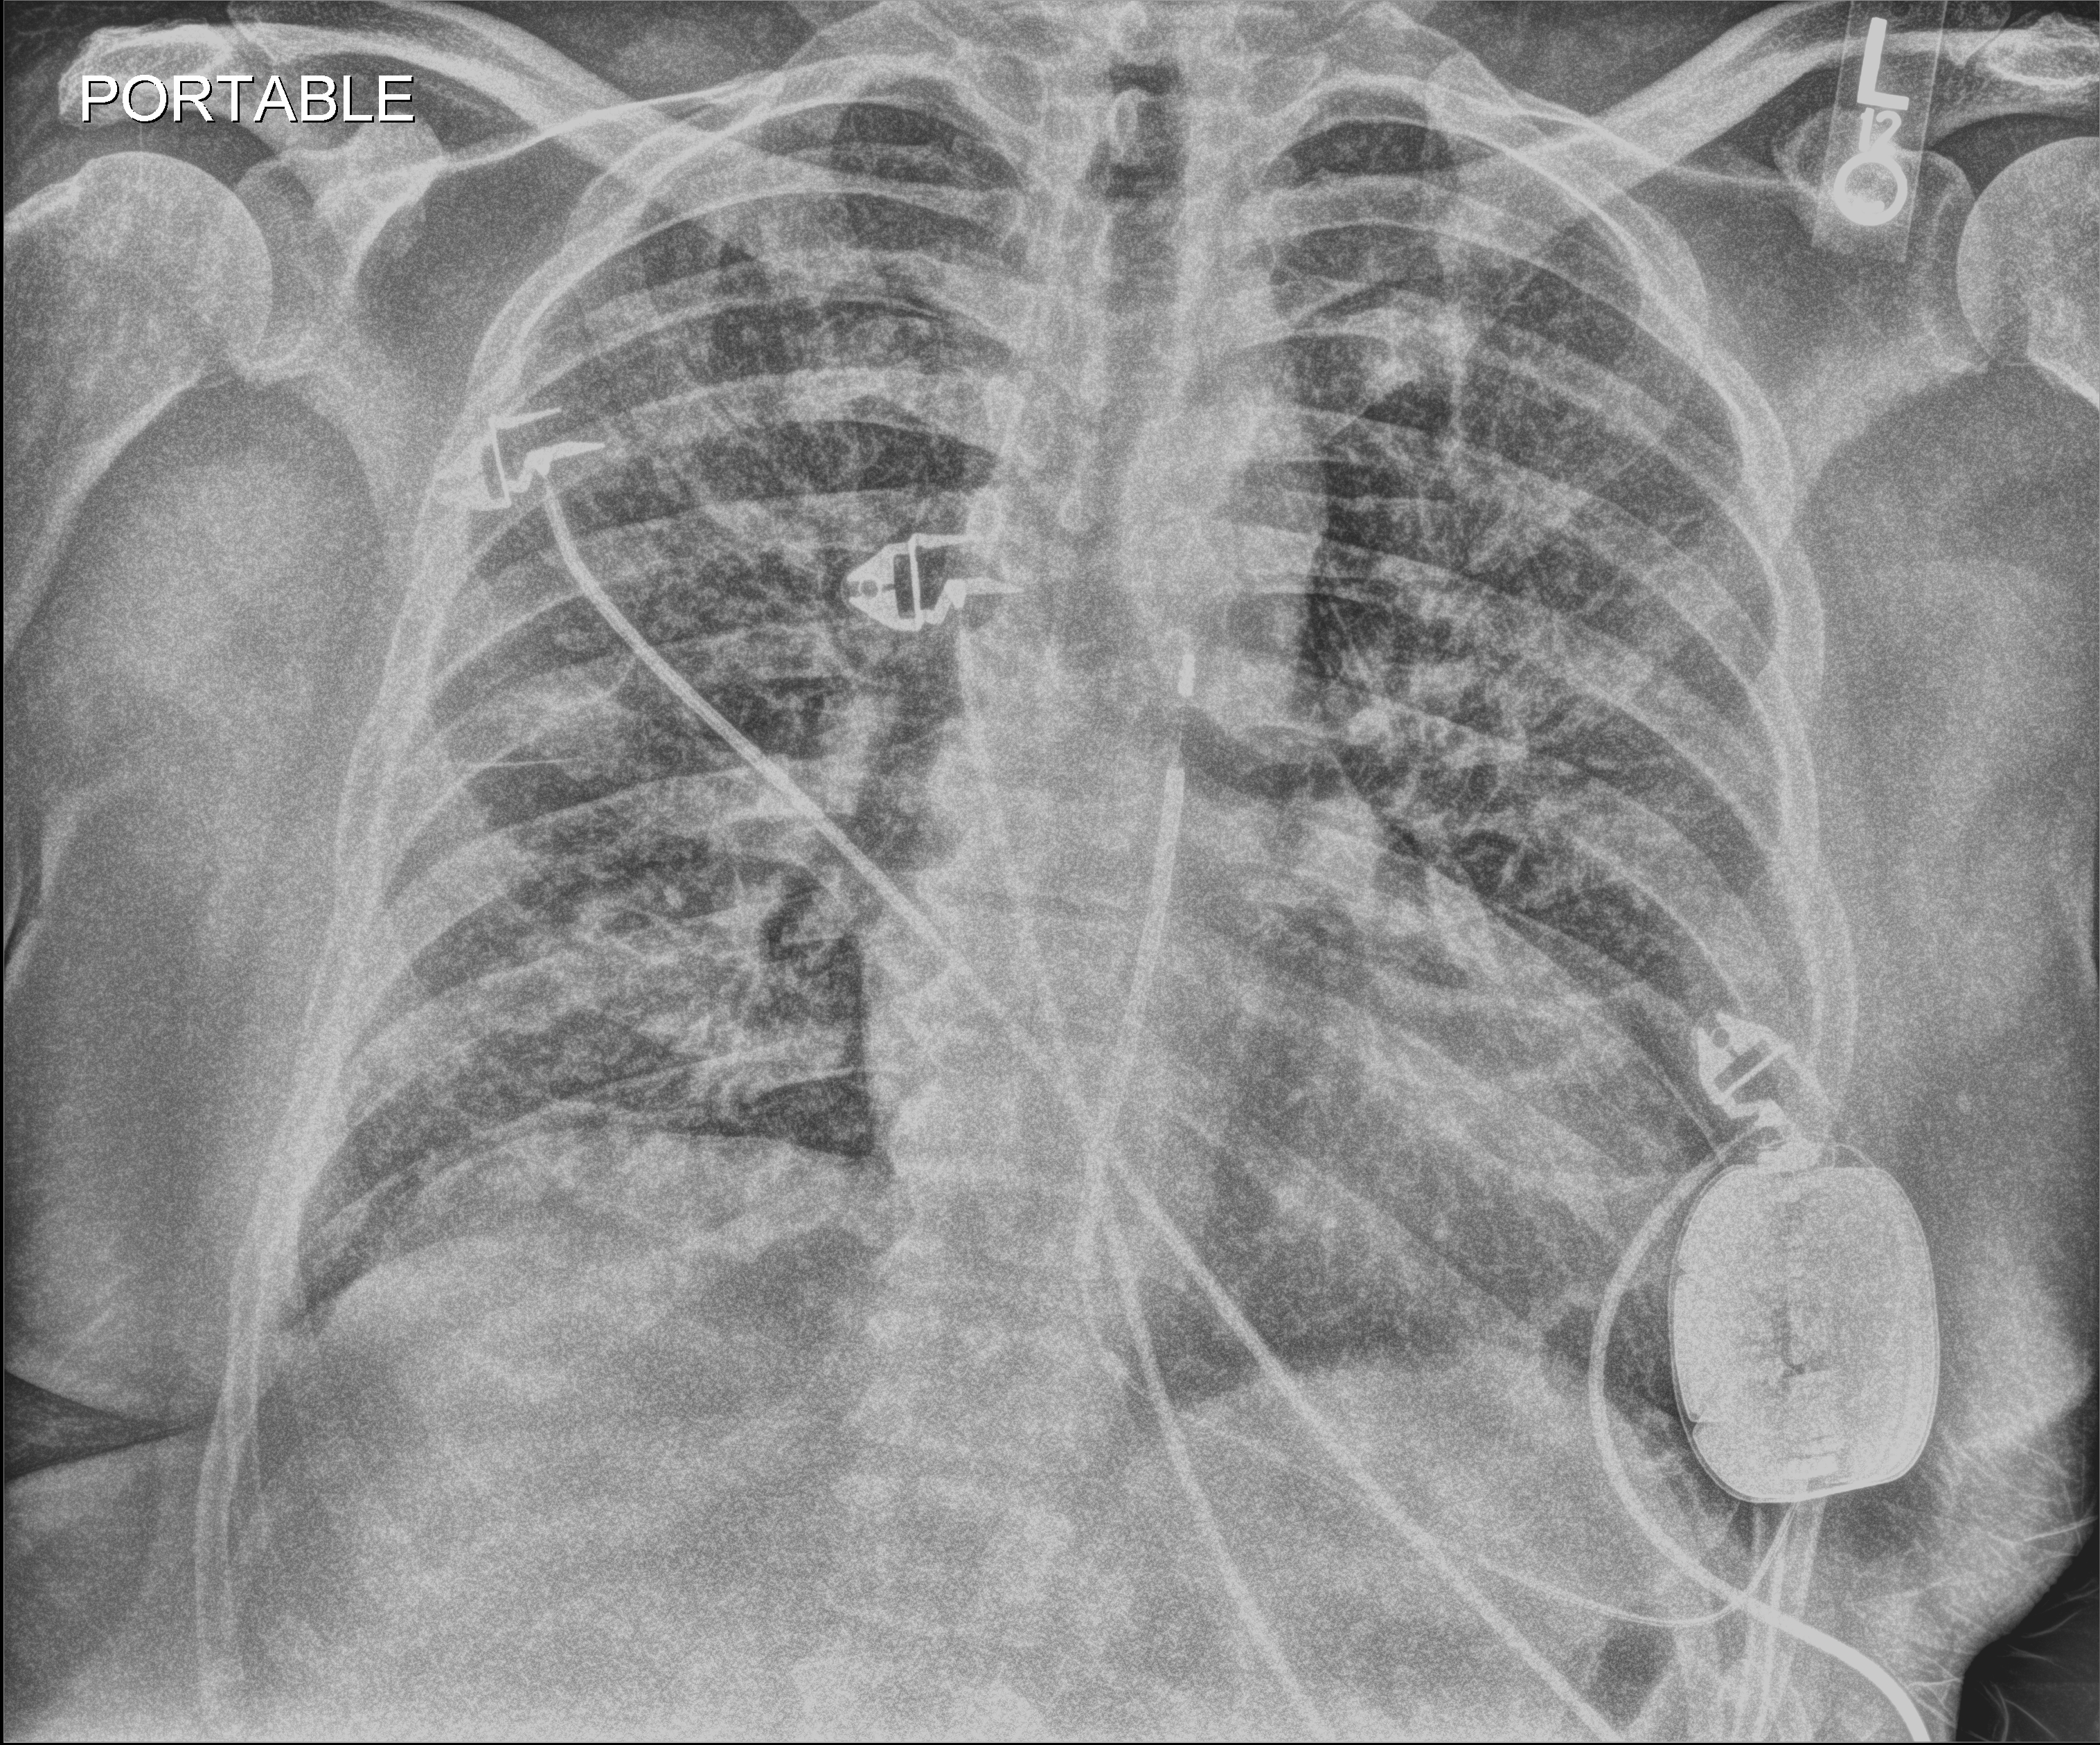
Bedside chest radiograph (digital radiography), anteroposterior (AP) projection. Patient hospitalised with COVID-19; male, aged 60–74 years.
Hospital-stay facts (about this admission, not read from this image; timing relative to this image not recorded):
- other chronic lung disease (admission record): no